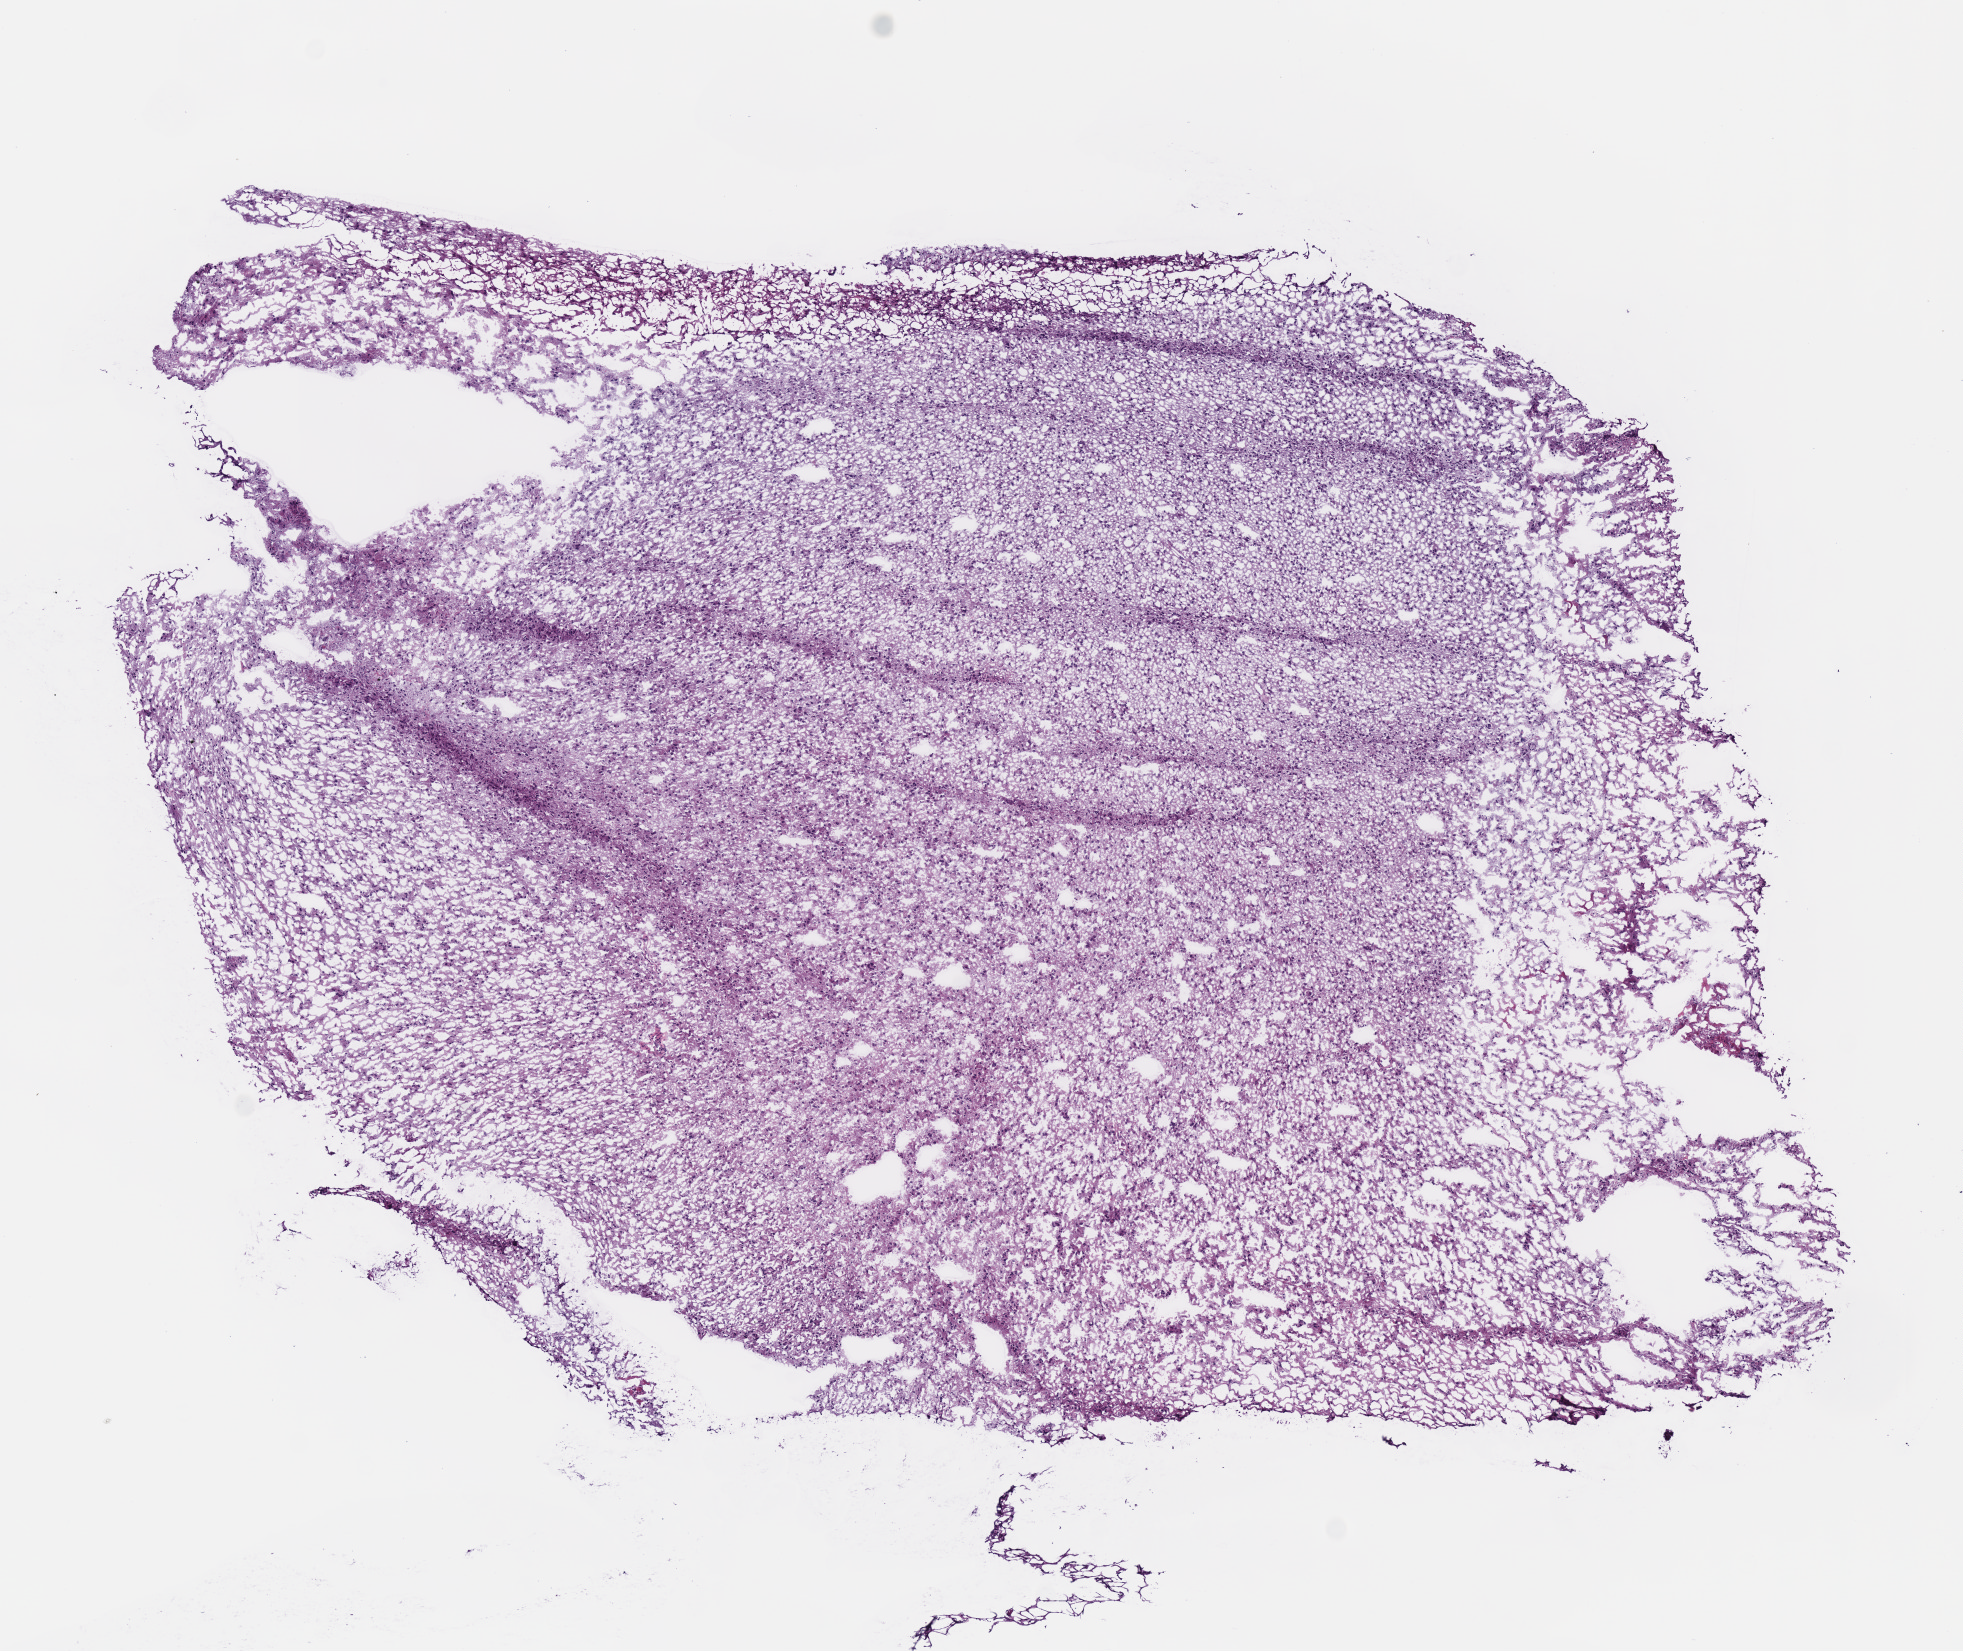
H&E-stained whole-slide image, low-resolution overview of the scanned area, about 7.7 x 6.5 mm (slide scanned at 40x). Frozen section from the top of the tissue portion. Brain, primary tumour sample. Male patient; age at initial diagnosis 34 years. Histologic grade: G3 (poorly differentiated). Pathologist review of this section (percent, as recorded): tumour cells 100%, tumour nuclei 80%, normal cells 0%, stromal cells 0%, necrosis 0%.
Histologic diagnosis: Mixed glioma (cerebrum).